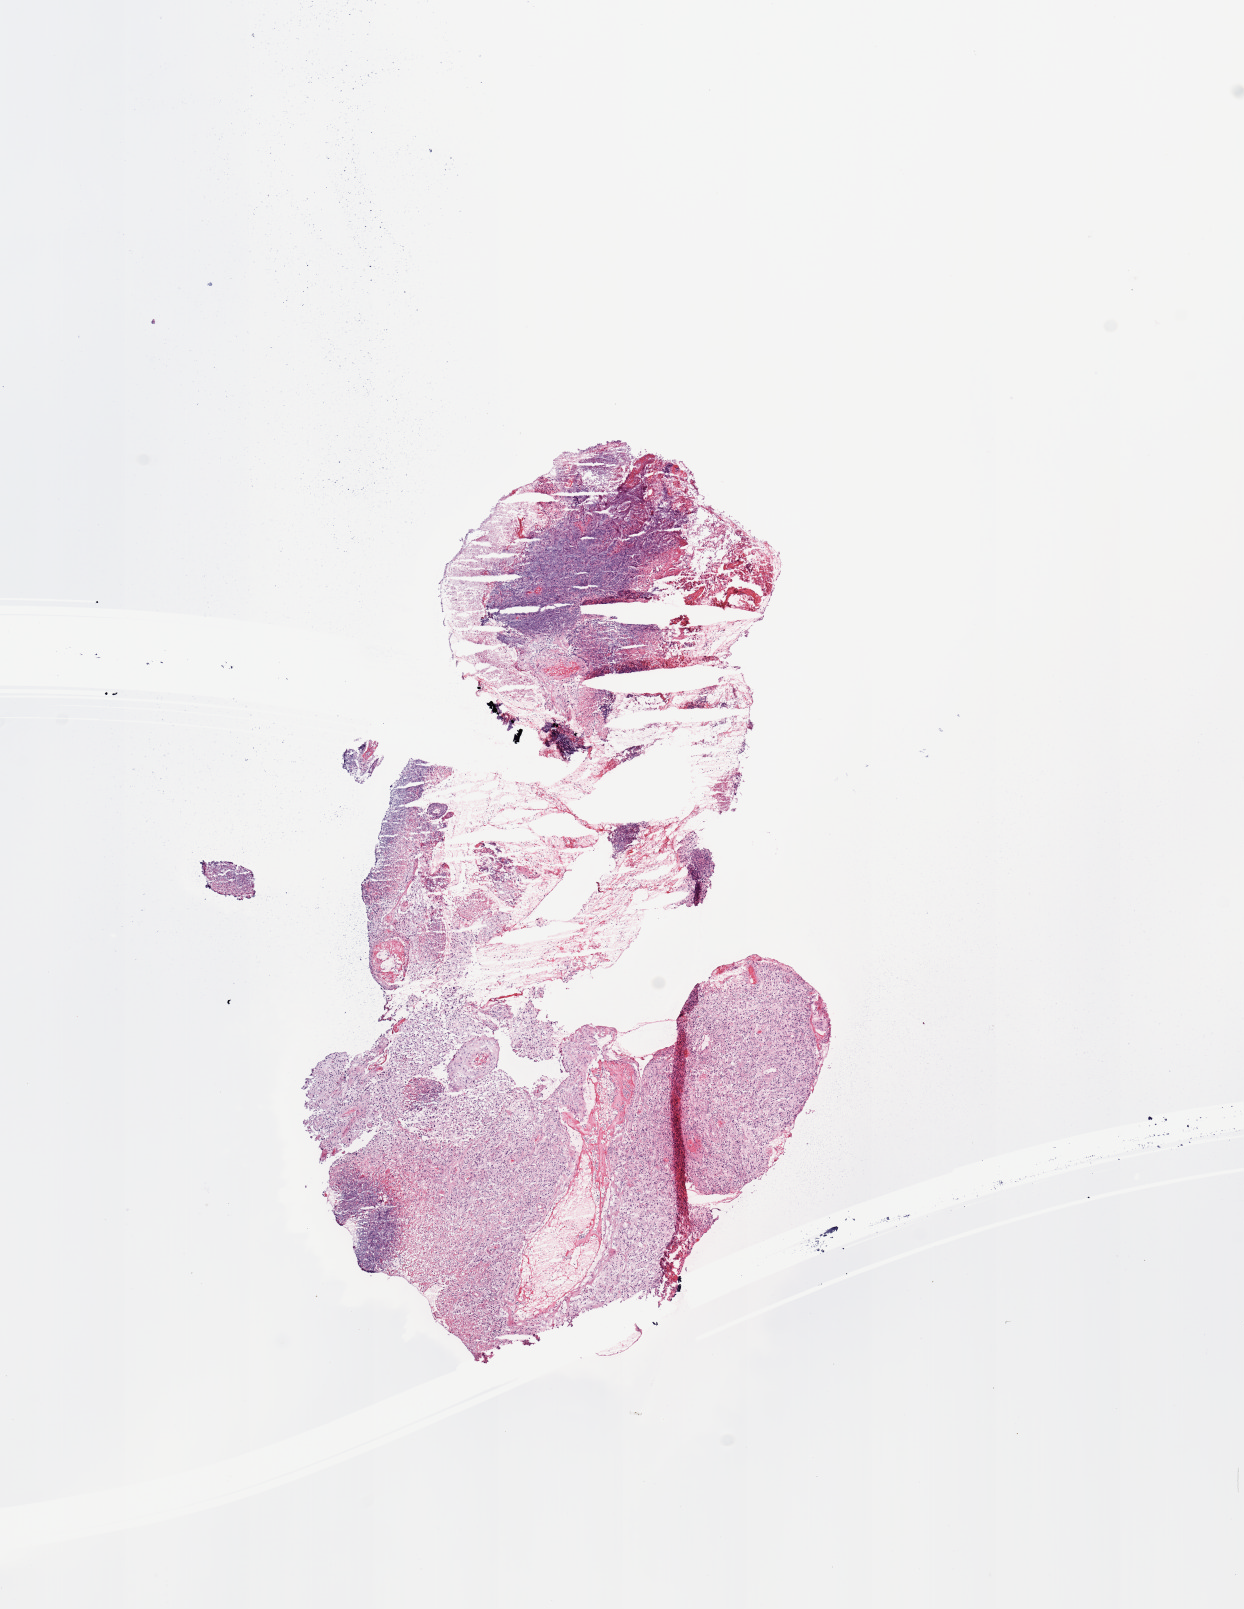
Whole-slide histology image, Hematoxylin and eosin (H&E) stained, shown as a low-resolution overview of the whole scanned area (about 9.8 x 12.7 mm, acquisition: 20x scan). Tumour tissue sample, brain. Patient: female, age 74 years.
• patient diagnosis (cohort enrolment): glioblastoma multiforme (brain)
• primary tumour site (as recorded): temporal lobe